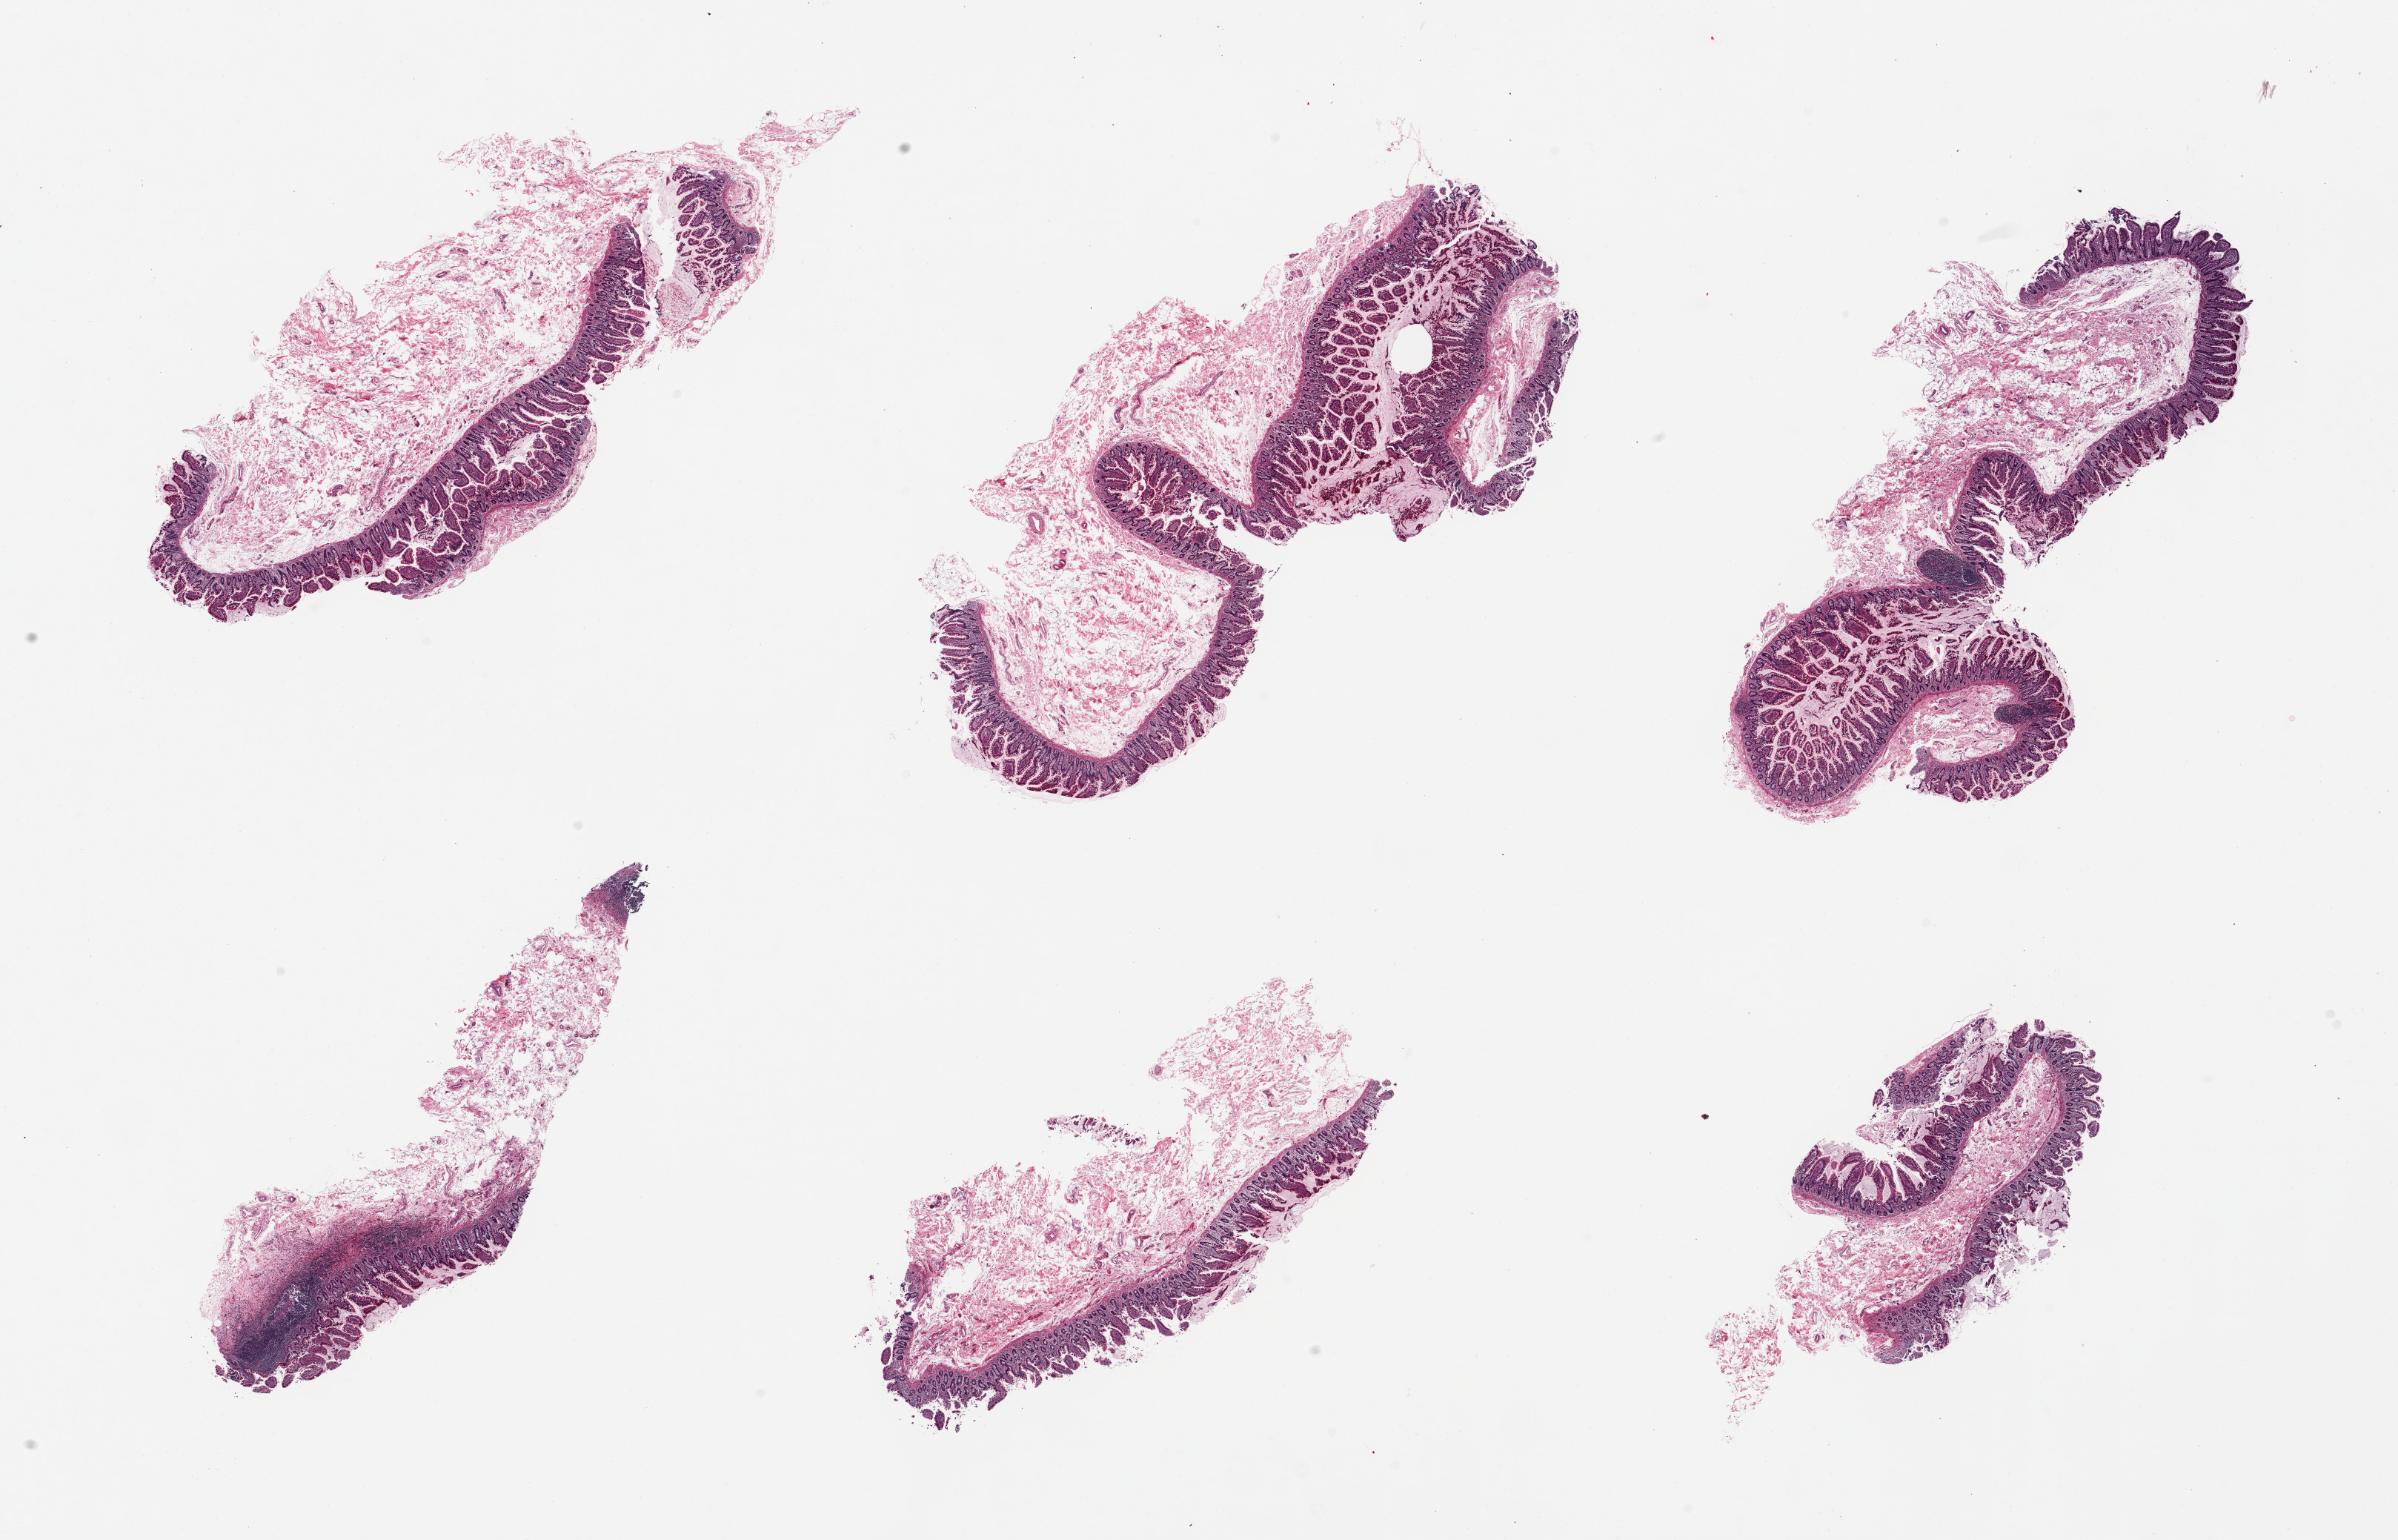
H&E whole-slide image, low-resolution overview of the scanned area, about 25.6 x 16.4 mm (slide scanned at 20x), PAXgene-fixed paraffin-embedded (PFPE) section, sampled site (target tissue): ileum, tissue donor sample. Donor: female.
Reviewer comment on this tissue sample: 6 pieces, wlle preserved mucosa; target lymphoid aggregates are ~10% tissue.